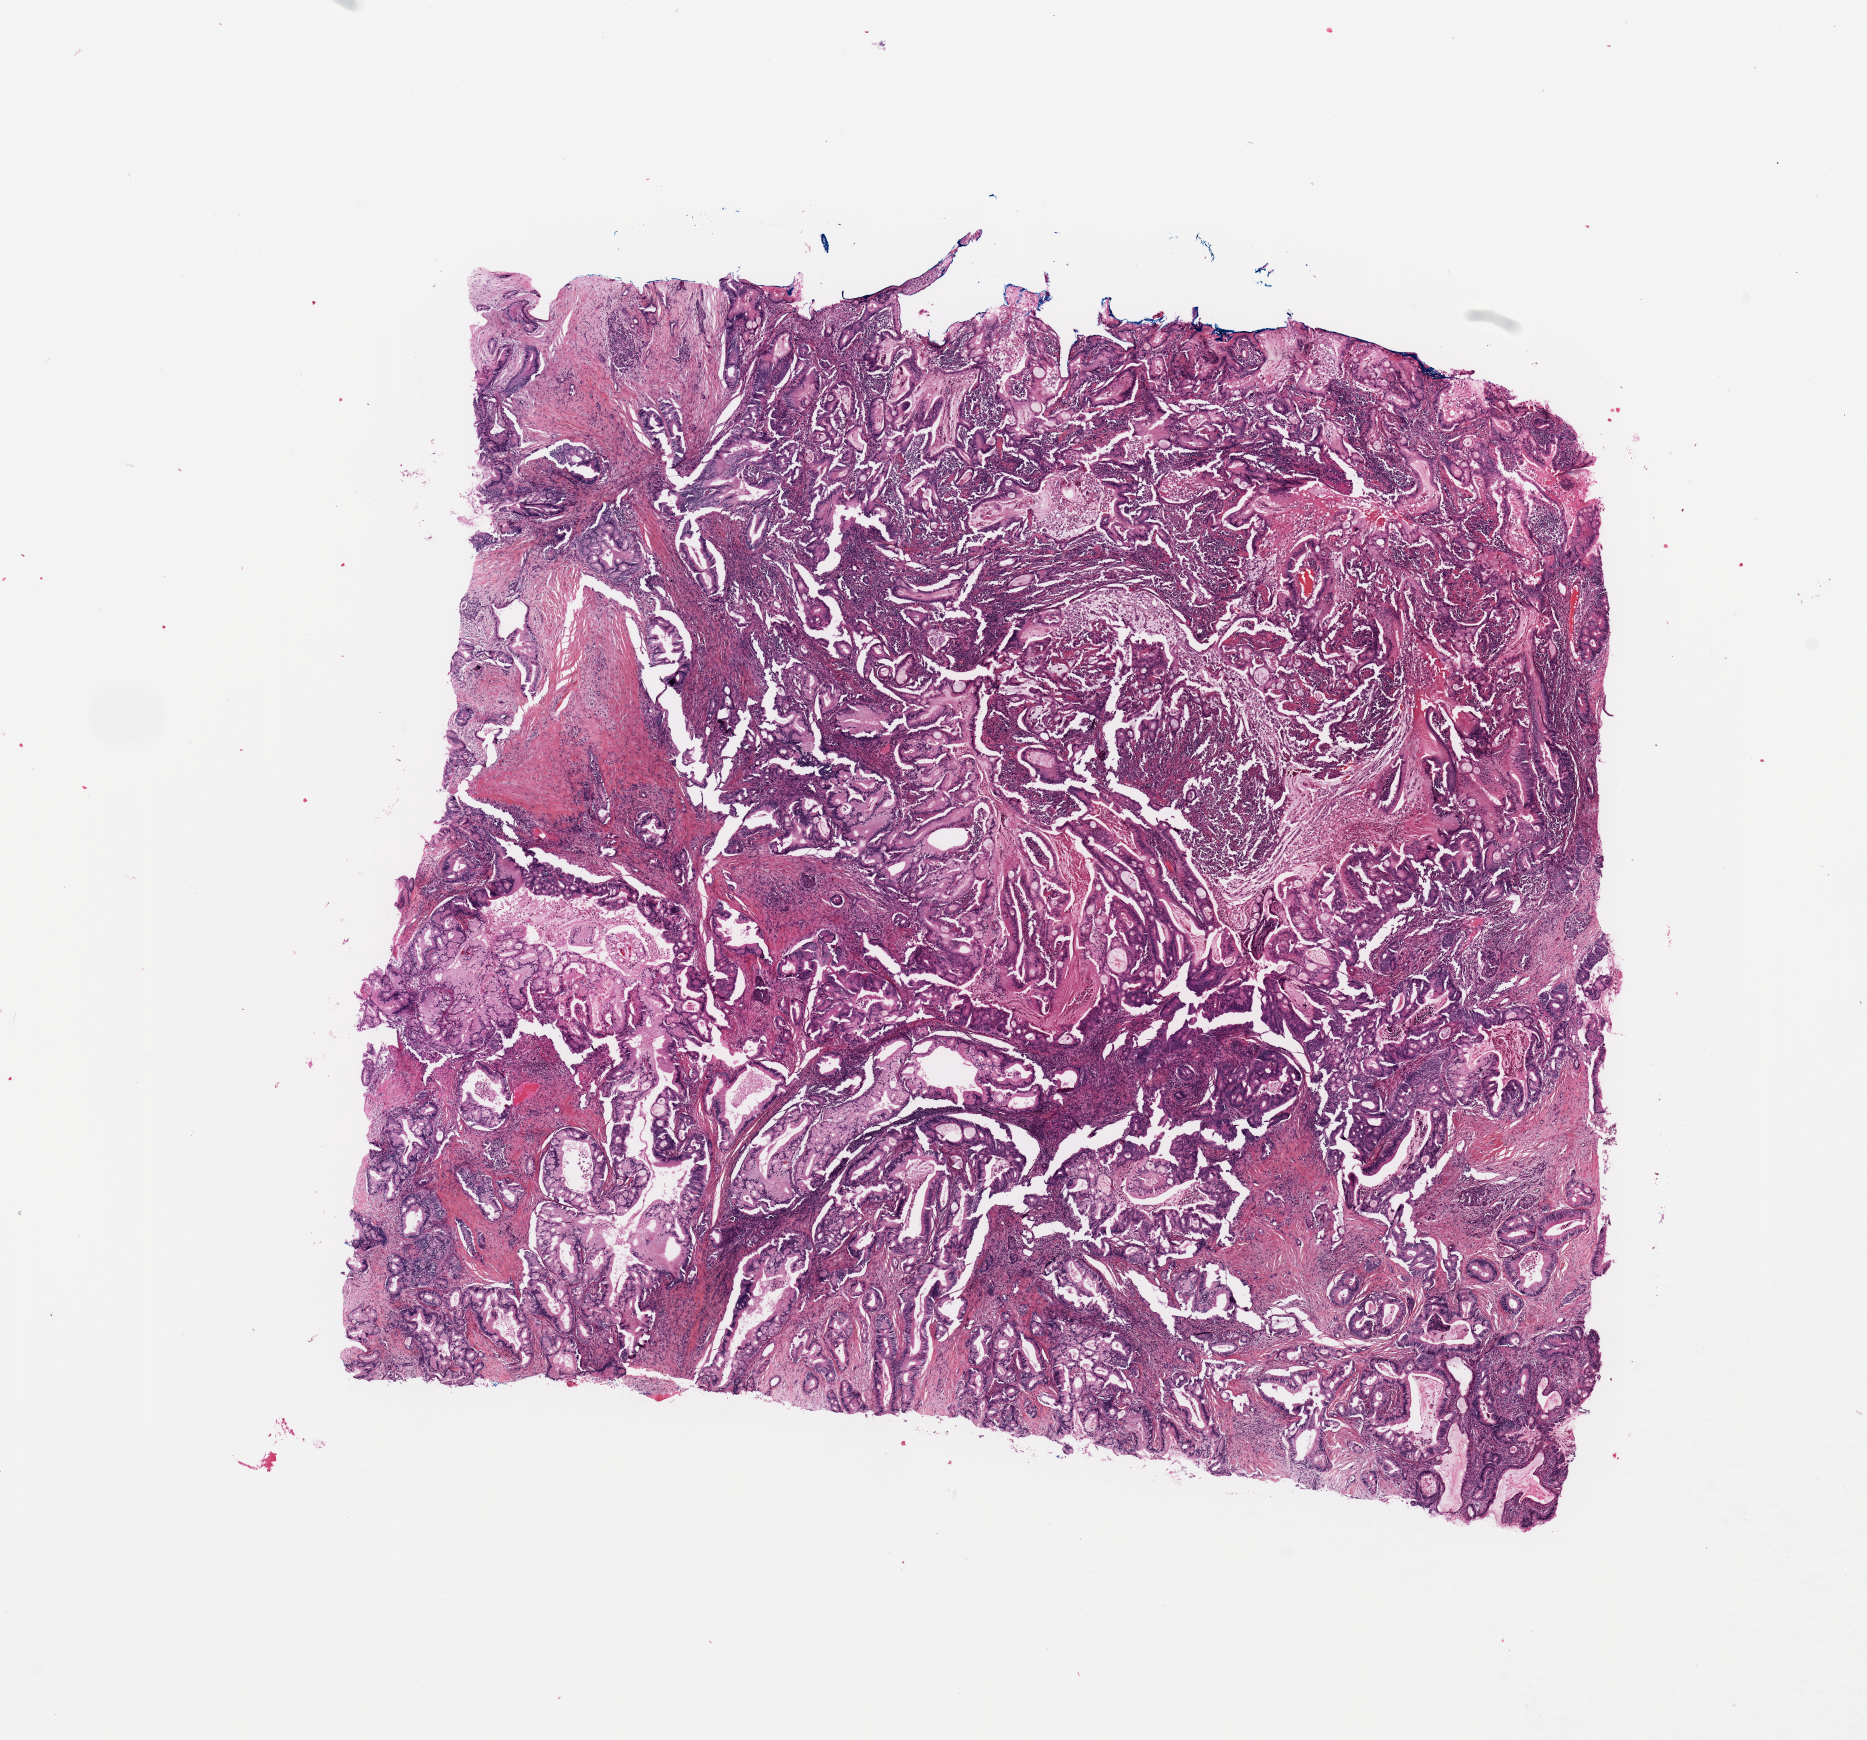
H&E whole-slide image, whole scanned area (about 14.8 x 13.8 mm) shown as a low-resolution overview; tumour tissue sample, sampled site: pancreas. Female, 64 y/o. Histologic grade: G2 (moderately differentiated). Slide review estimates, as recorded: tumour nuclei 80%, necrosis 5%.
Histologic diagnosis: Infiltrating duct carcinoma, NOS. AJCC pathologic stage: IIA.